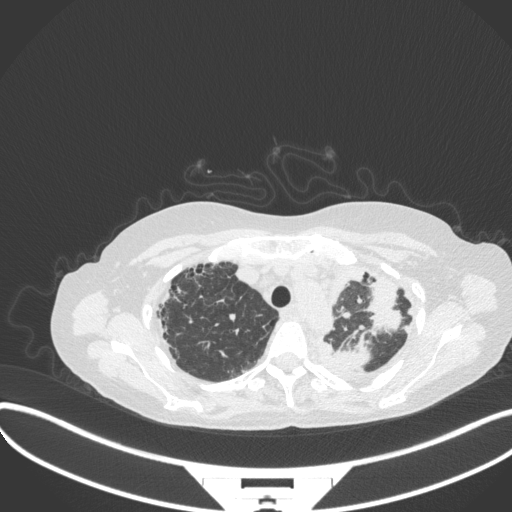
Chest CT, one axial slice; position 273 of 373 along the scan axis; reconstruction kernel B31f; 120 kVp; lung window (W 1500 / L -600 HU); 1 mm slice thickness; 512 × 512 image matrix, field of view 400 × 400 mm. Female patient, age 56 years. From the clinical record (not read from this slice): clinical TNM (as recorded): T1 N0 M0.
Structures marked on this image (bounding box drawn by a radiologist):
- lung tumour (recorded histology: adenocarcinoma): box from (x=336, y=336) to (x=374, y=373) px
- lung tumour (recorded histology: adenocarcinoma): (x=365, y=272)–(x=409, y=336)